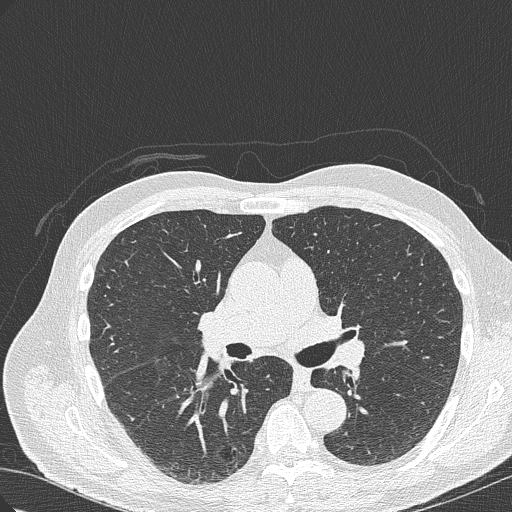
Axial slice from a low-dose chest CT screening exam. First (baseline) screen. Lung window (W 1500 / L -600 HU). 1 mm slice thickness. 120 kVp. Slice 134 of 322 in the series. Male, age 70 years at enrolment. Current smoker at enrolment.
Lesion marked by an expert reader, bounding box <199,419,262,475> (left, top, right, bottom; pixels). The screening reader recorded 4 non-calcified nodules or masses ≥4 mm on this exam; which of them this box marks is not recorded. Participant outcome: lung cancer diagnosed 978 days after this screen — bronchiolo-alveolar adenocarcinoma, NOS, right lower lobe, poorly differentiated (G3), stage IB (AJCC 6th edition), 30 mm at pathology.